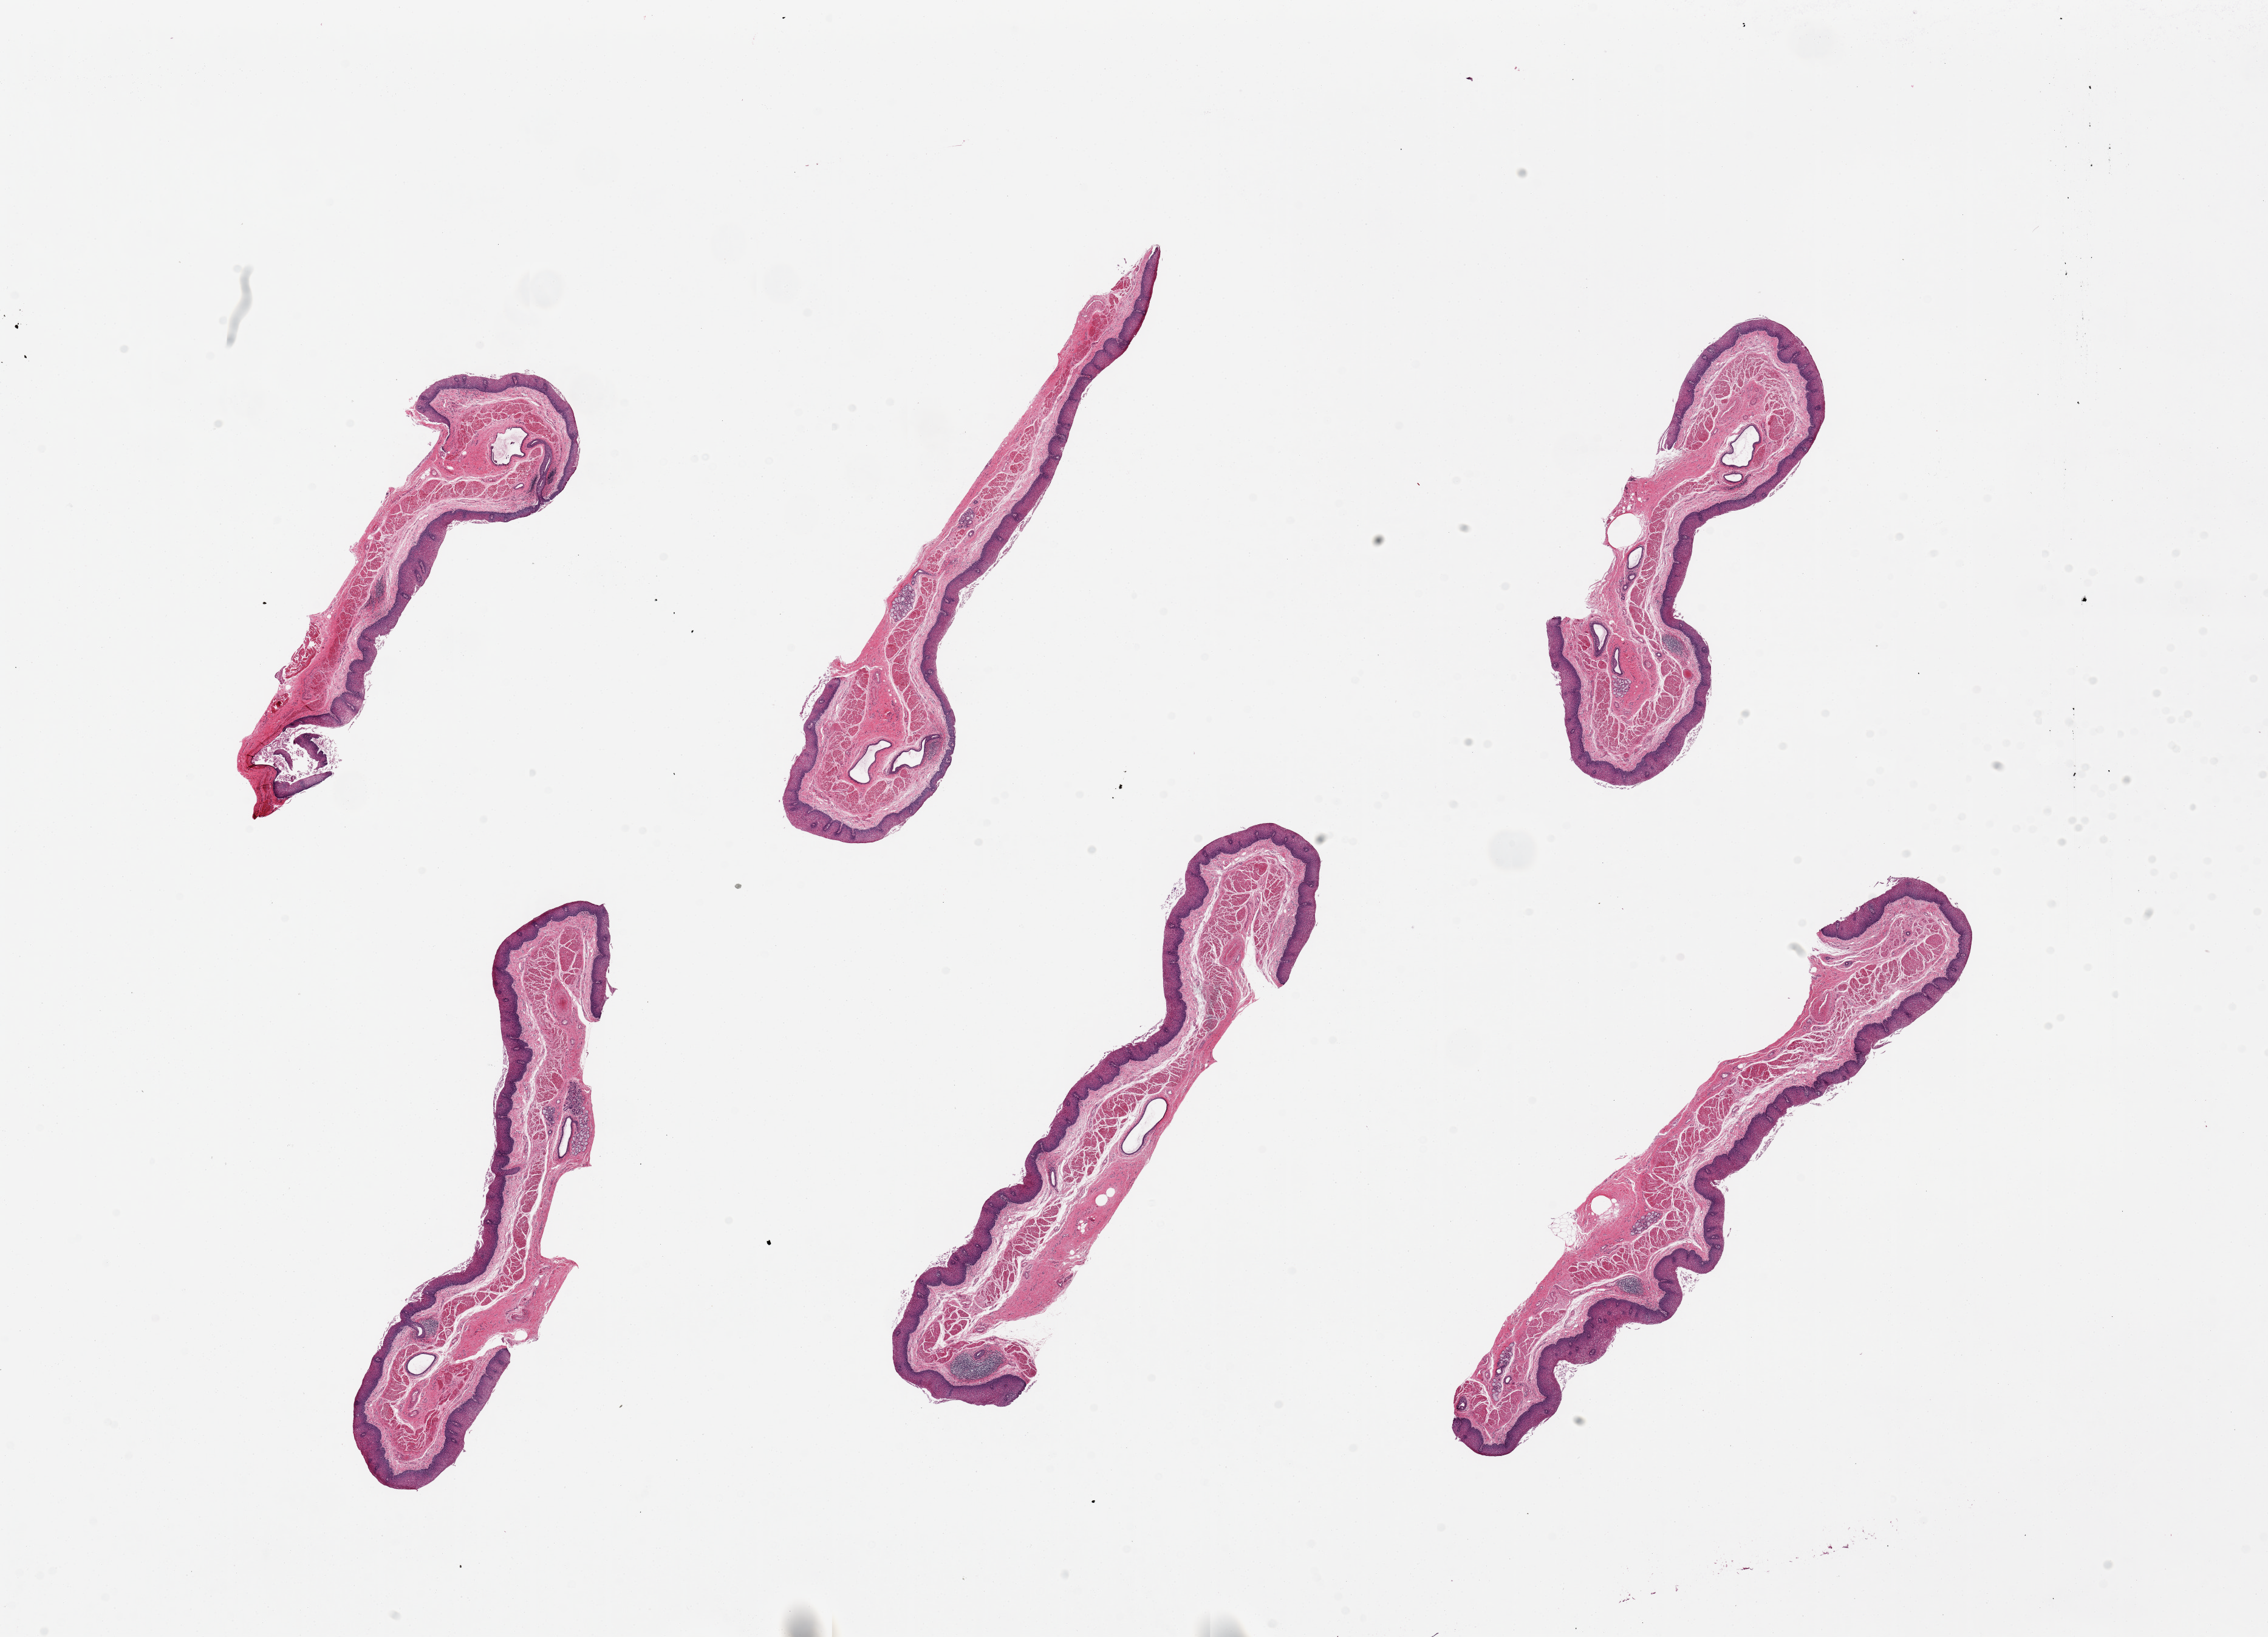
Whole-slide image, haematoxylin and eosin stain, whole scanned area (about 29.5 x 21.3 mm, acquisition: 20x scan) shown as a low-resolution overview; PAXgene-fixed paraffin-embedded (PFPE) section; section of esophageal mucous membrane (target tissue); tissue donor sample. Donor: female.
• review note (as recorded): 6 pieces, up to 10x2mm; squamous mucosa is ~10-15% of thickness